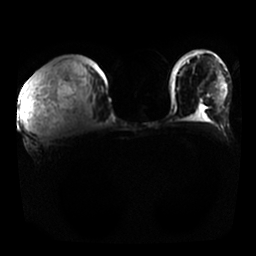
Breast MRI, one axial slice. Diffusion-weighted series; image 2 of 4 stored at this slice position (different b-values; order by instance number). 1.5 T. 256 × 256 image matrix, field of view 350 × 350 mm. Female patient.
Outlined on this slice (manually delineated by an expert):
- tumour on diffusion-weighted imaging: bounding box (x1, y1, x2, y2) in pixels: (21, 95, 41, 134)